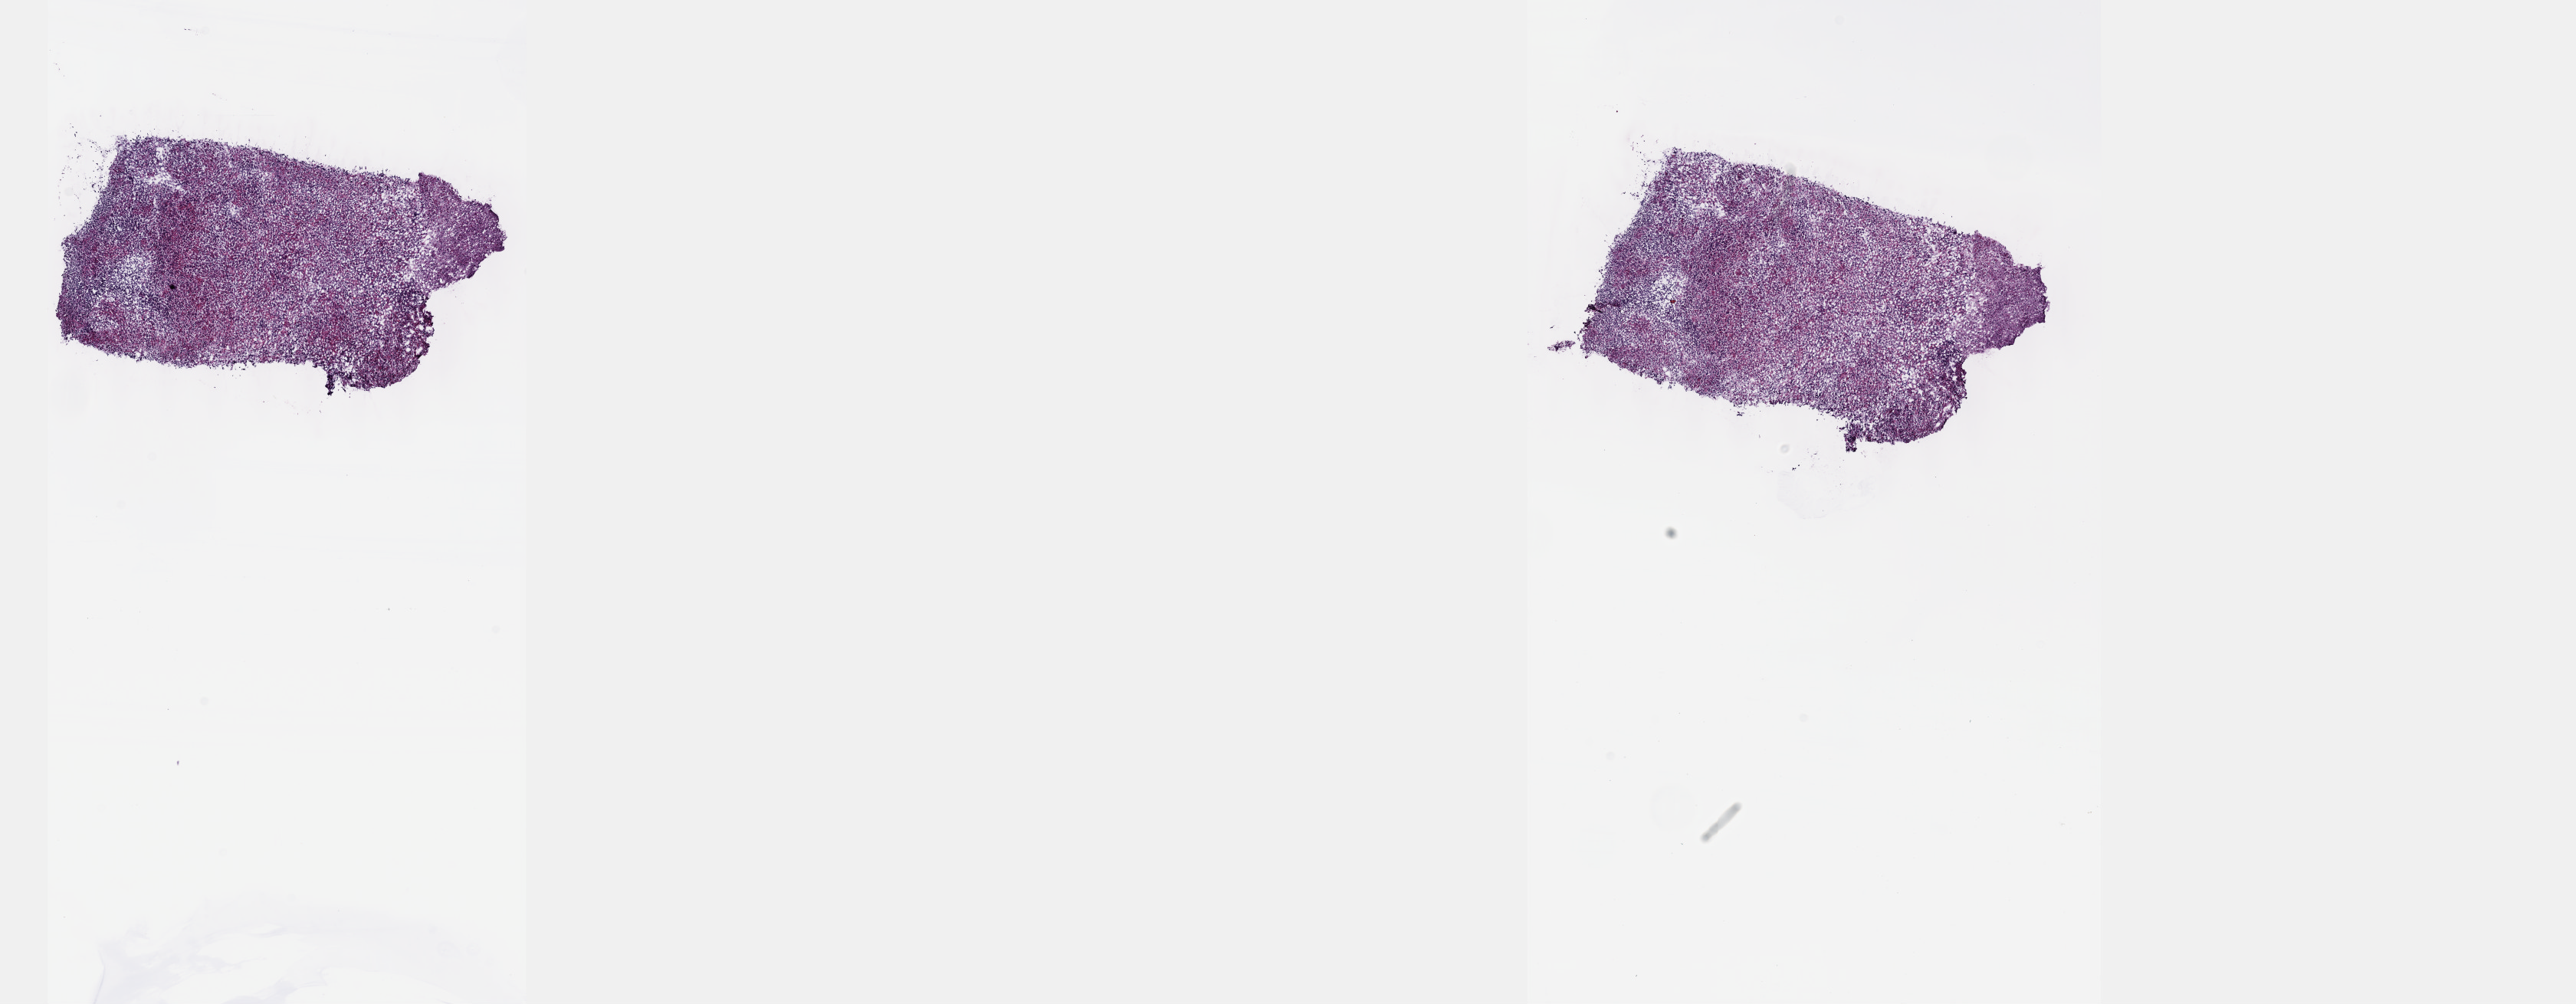
Hematoxylin and eosin (H&E) stained whole-slide image — low-resolution overview of the scanned area, about 27.2 x 10.6 mm (slide scanned at 40x). Frozen section from the top of the tissue portion. Brain, primary tumour sample. Male, age 30 years at initial diagnosis. Pathologist review of this section (percent, as recorded): tumour cells 80%, tumour nuclei 90%.
Diagnosis: Astrocytoma, anaplastic.